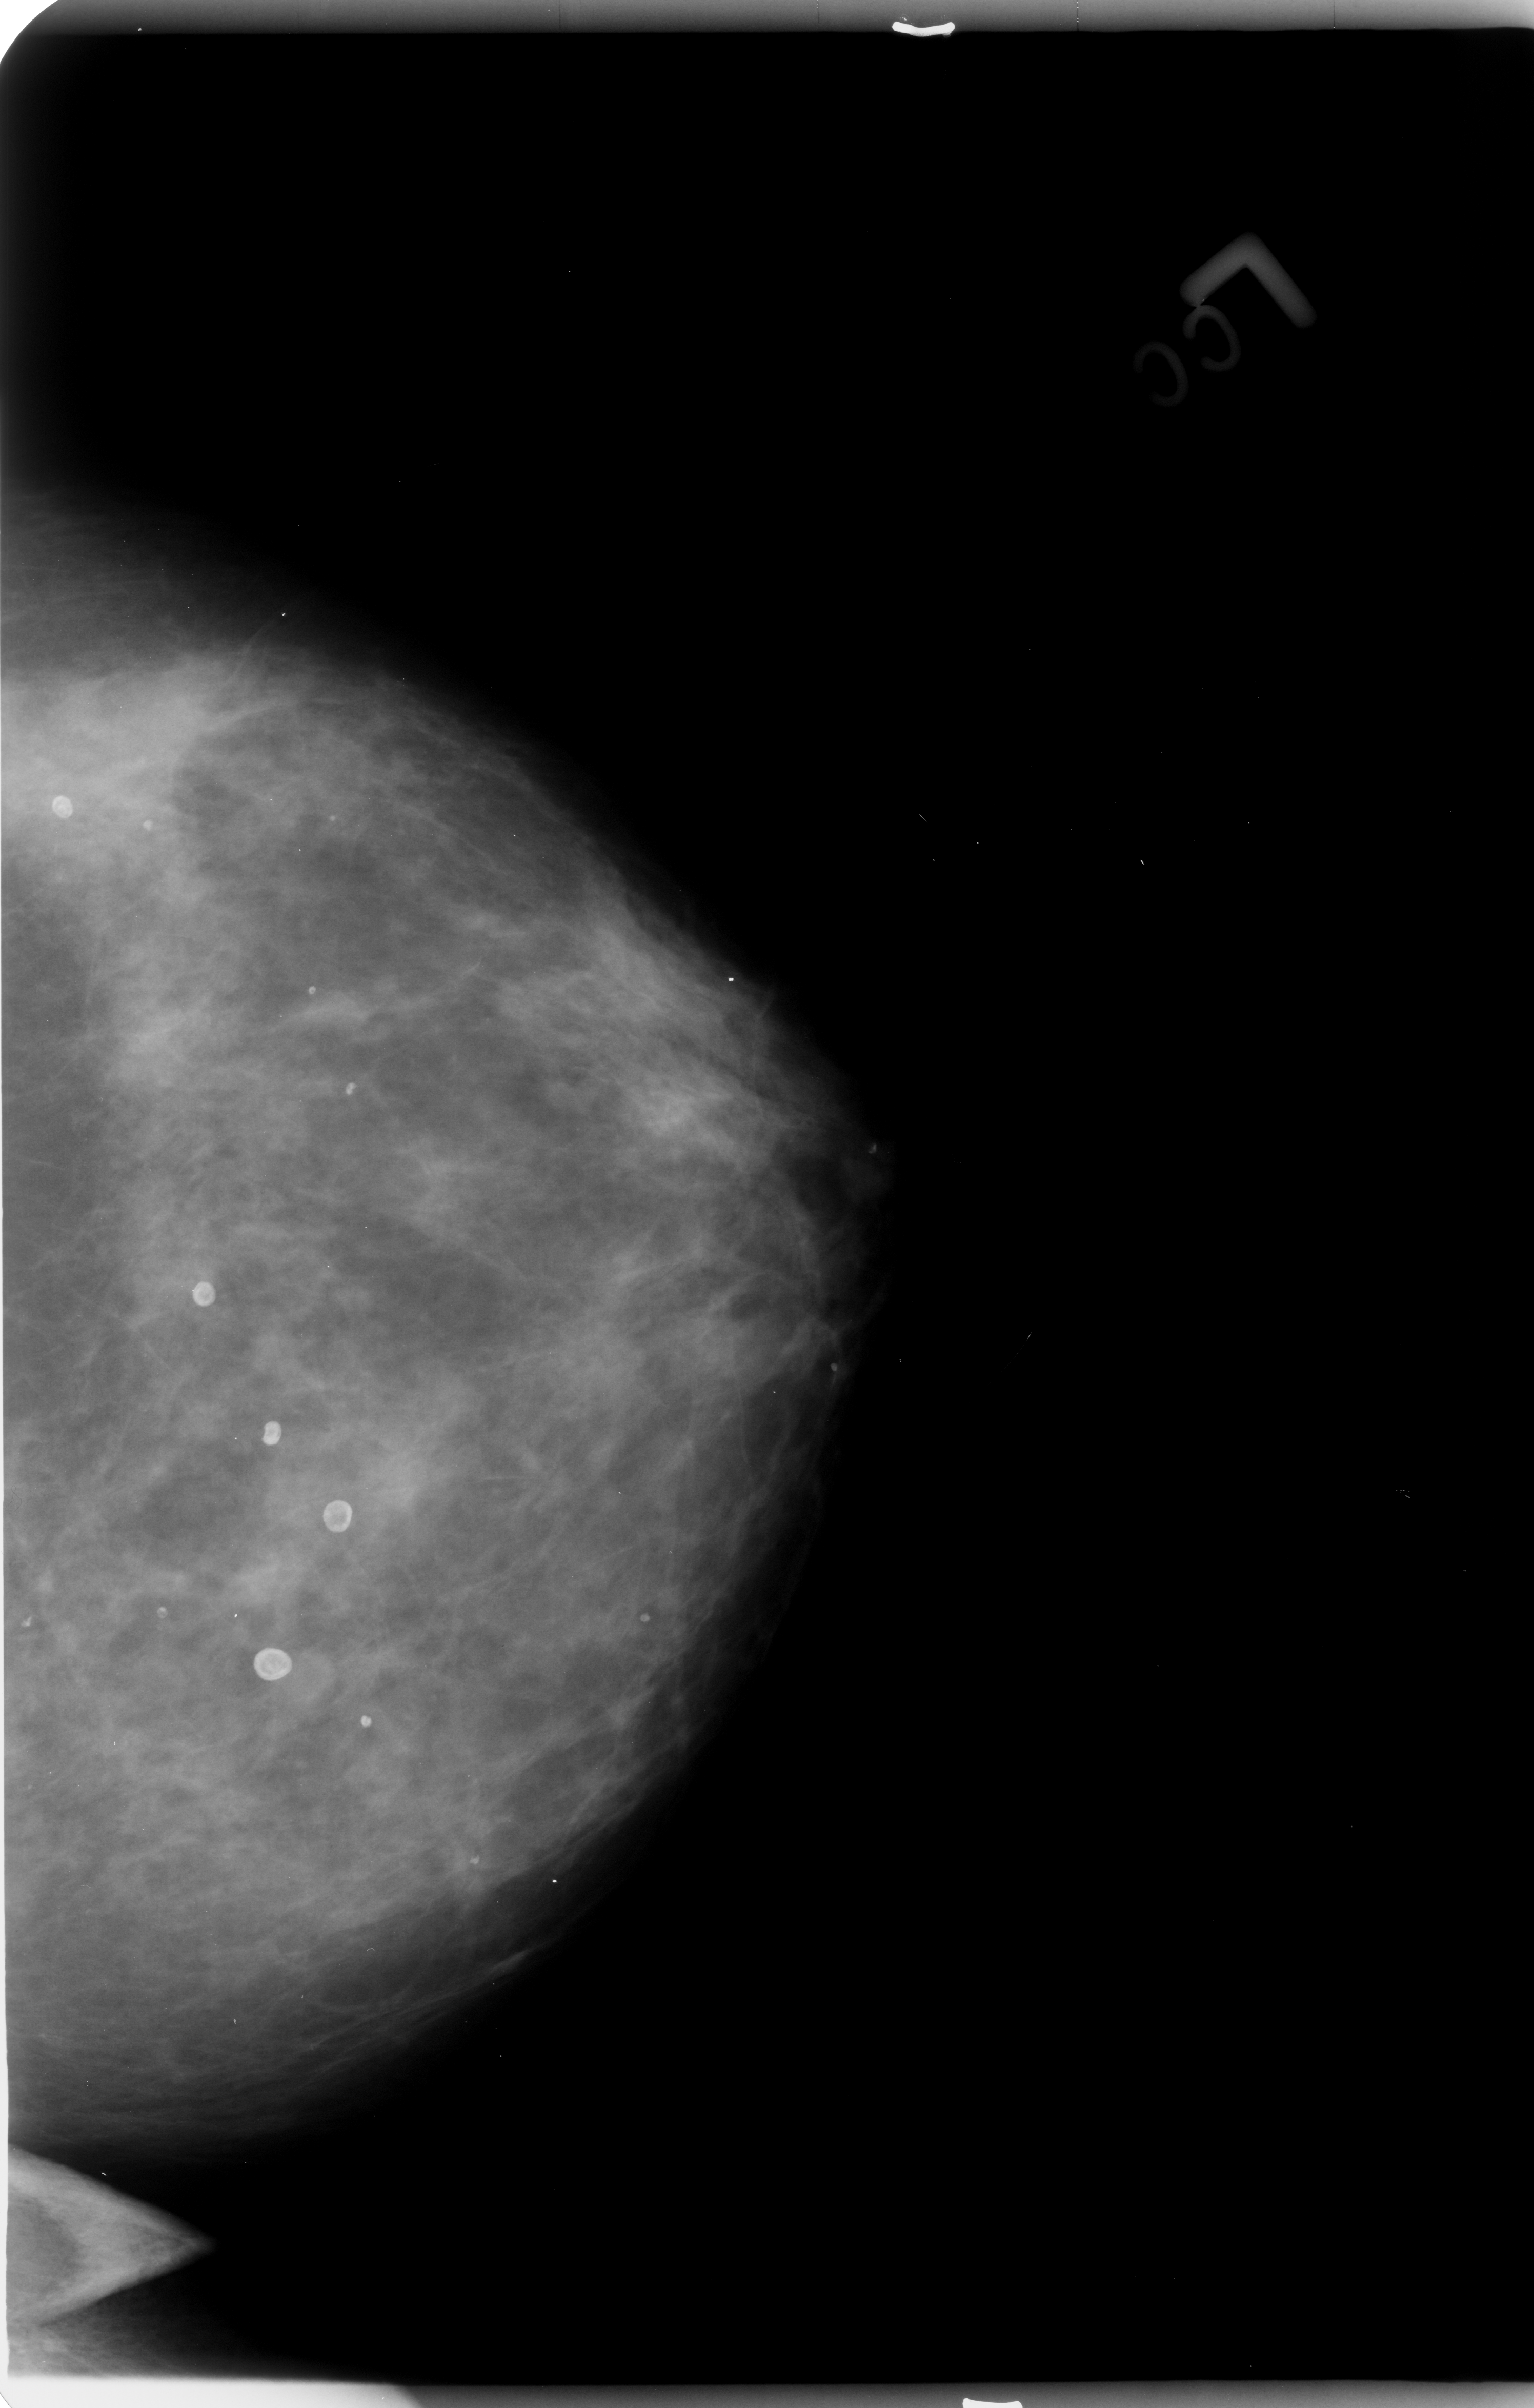
Scanned film-screen mammogram, left breast, CC view, BI-RADS breast density category 3 (scale 1–4).
Radiologist-marked abnormalities on this image: Finding 1 of 4: calcifications, morphology round and regular / eggshell; BI-RADS assessment category 2; subtlety rating 3 on a 1 (subtle) to 5 (obvious) scale; benign; no additional work-up was recommended (benign without callback). Finding 2 of 4: calcifications, morphology round and regular / eggshell; BI-RADS assessment category 2; benign; no additional work-up was recommended (benign without callback). Finding 3 of 4: calcifications, morphology round and regular / eggshell; BI-RADS assessment category 2; subtlety rating 3 on a 1 (subtle) to 5 (obvious) scale; benign without callback (not worked up further). Finding 4 of 4: calcifications, morphology round and regular / eggshell; BI-RADS assessment category 2; subtlety rating 3 on a 1 (subtle) to 5 (obvious) scale; benign without callback (not worked up further).